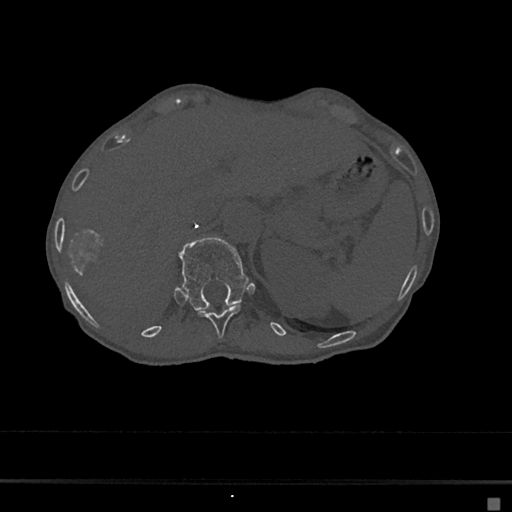
CT including the spine, one axial slice; position 141 of 797 along the scan axis; bone window (W 1800 / L 400 HU); 0.5 mm slice thickness; 512 × 512 image matrix. Patient: female, 68 years. From the clinical record (not read from this slice): primary cancer: renal.
Annotated regions visible in this slice (semi-automatic segmentation, software-assisted and operator-edited):
- T11 vertebra: bounding box (x1, y1, x2, y2) in pixels: (197, 305, 242, 338)
- T12 vertebra: (179, 237, 249, 311)